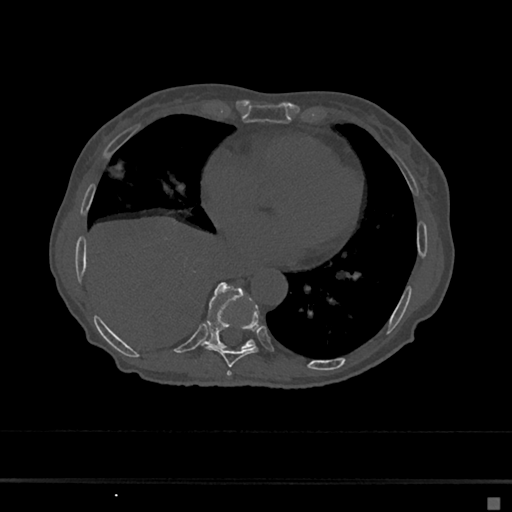
CT including the spine, one axial slice. Reconstruction kernel Br40s/3. 120 kVp. Bone window (W 1800 / L 400 HU). 512 × 512 image matrix, field of view 360 × 360 mm. Female patient, age 68 years. Case-level facts recorded for this patient, not image findings: primary cancer: renal.
Annotated regions visible in this slice (semi-automatic segmentation, software-assisted and operator-edited):
- T7 vertebra: bounding box <227,371,232,376> (left, top, right, bottom; pixels)
- T8 vertebra: <205,306,260,367>
- T9 vertebra: <205,282,255,349>